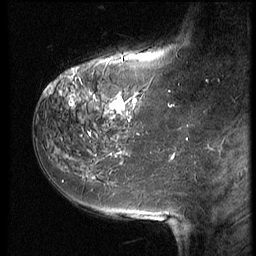
Breast MRI (dynamic contrast-enhanced), one sagittal slice; slice 18 of 64 in the series (ordered by position); 3 images stored at this slice position (order not interpretable as contrast timing); 1.5 T; TE 4.2 ms, TR 9 ms; 256 × 256 image matrix, field of view 180 × 180 mm. Patient: female, 59 years. Case-level facts recorded for this patient, not image findings: setting: breast cancer imaged before/during neoadjuvant chemotherapy; receptor status: HER2-positive.
Structures marked on this image (semi-automatic segmentation, software-assisted and operator-edited):
- analysis volume of interest (the breast-tissue region the enhancement analysis was run in; not a lesion): bounding box [x1, y1, x2, y2] px = [54, 65, 155, 132]
- tumour enhancement mask (voxels above the 140 % enhancement threshold inside the analysis volume of interest): [62, 71, 142, 120]